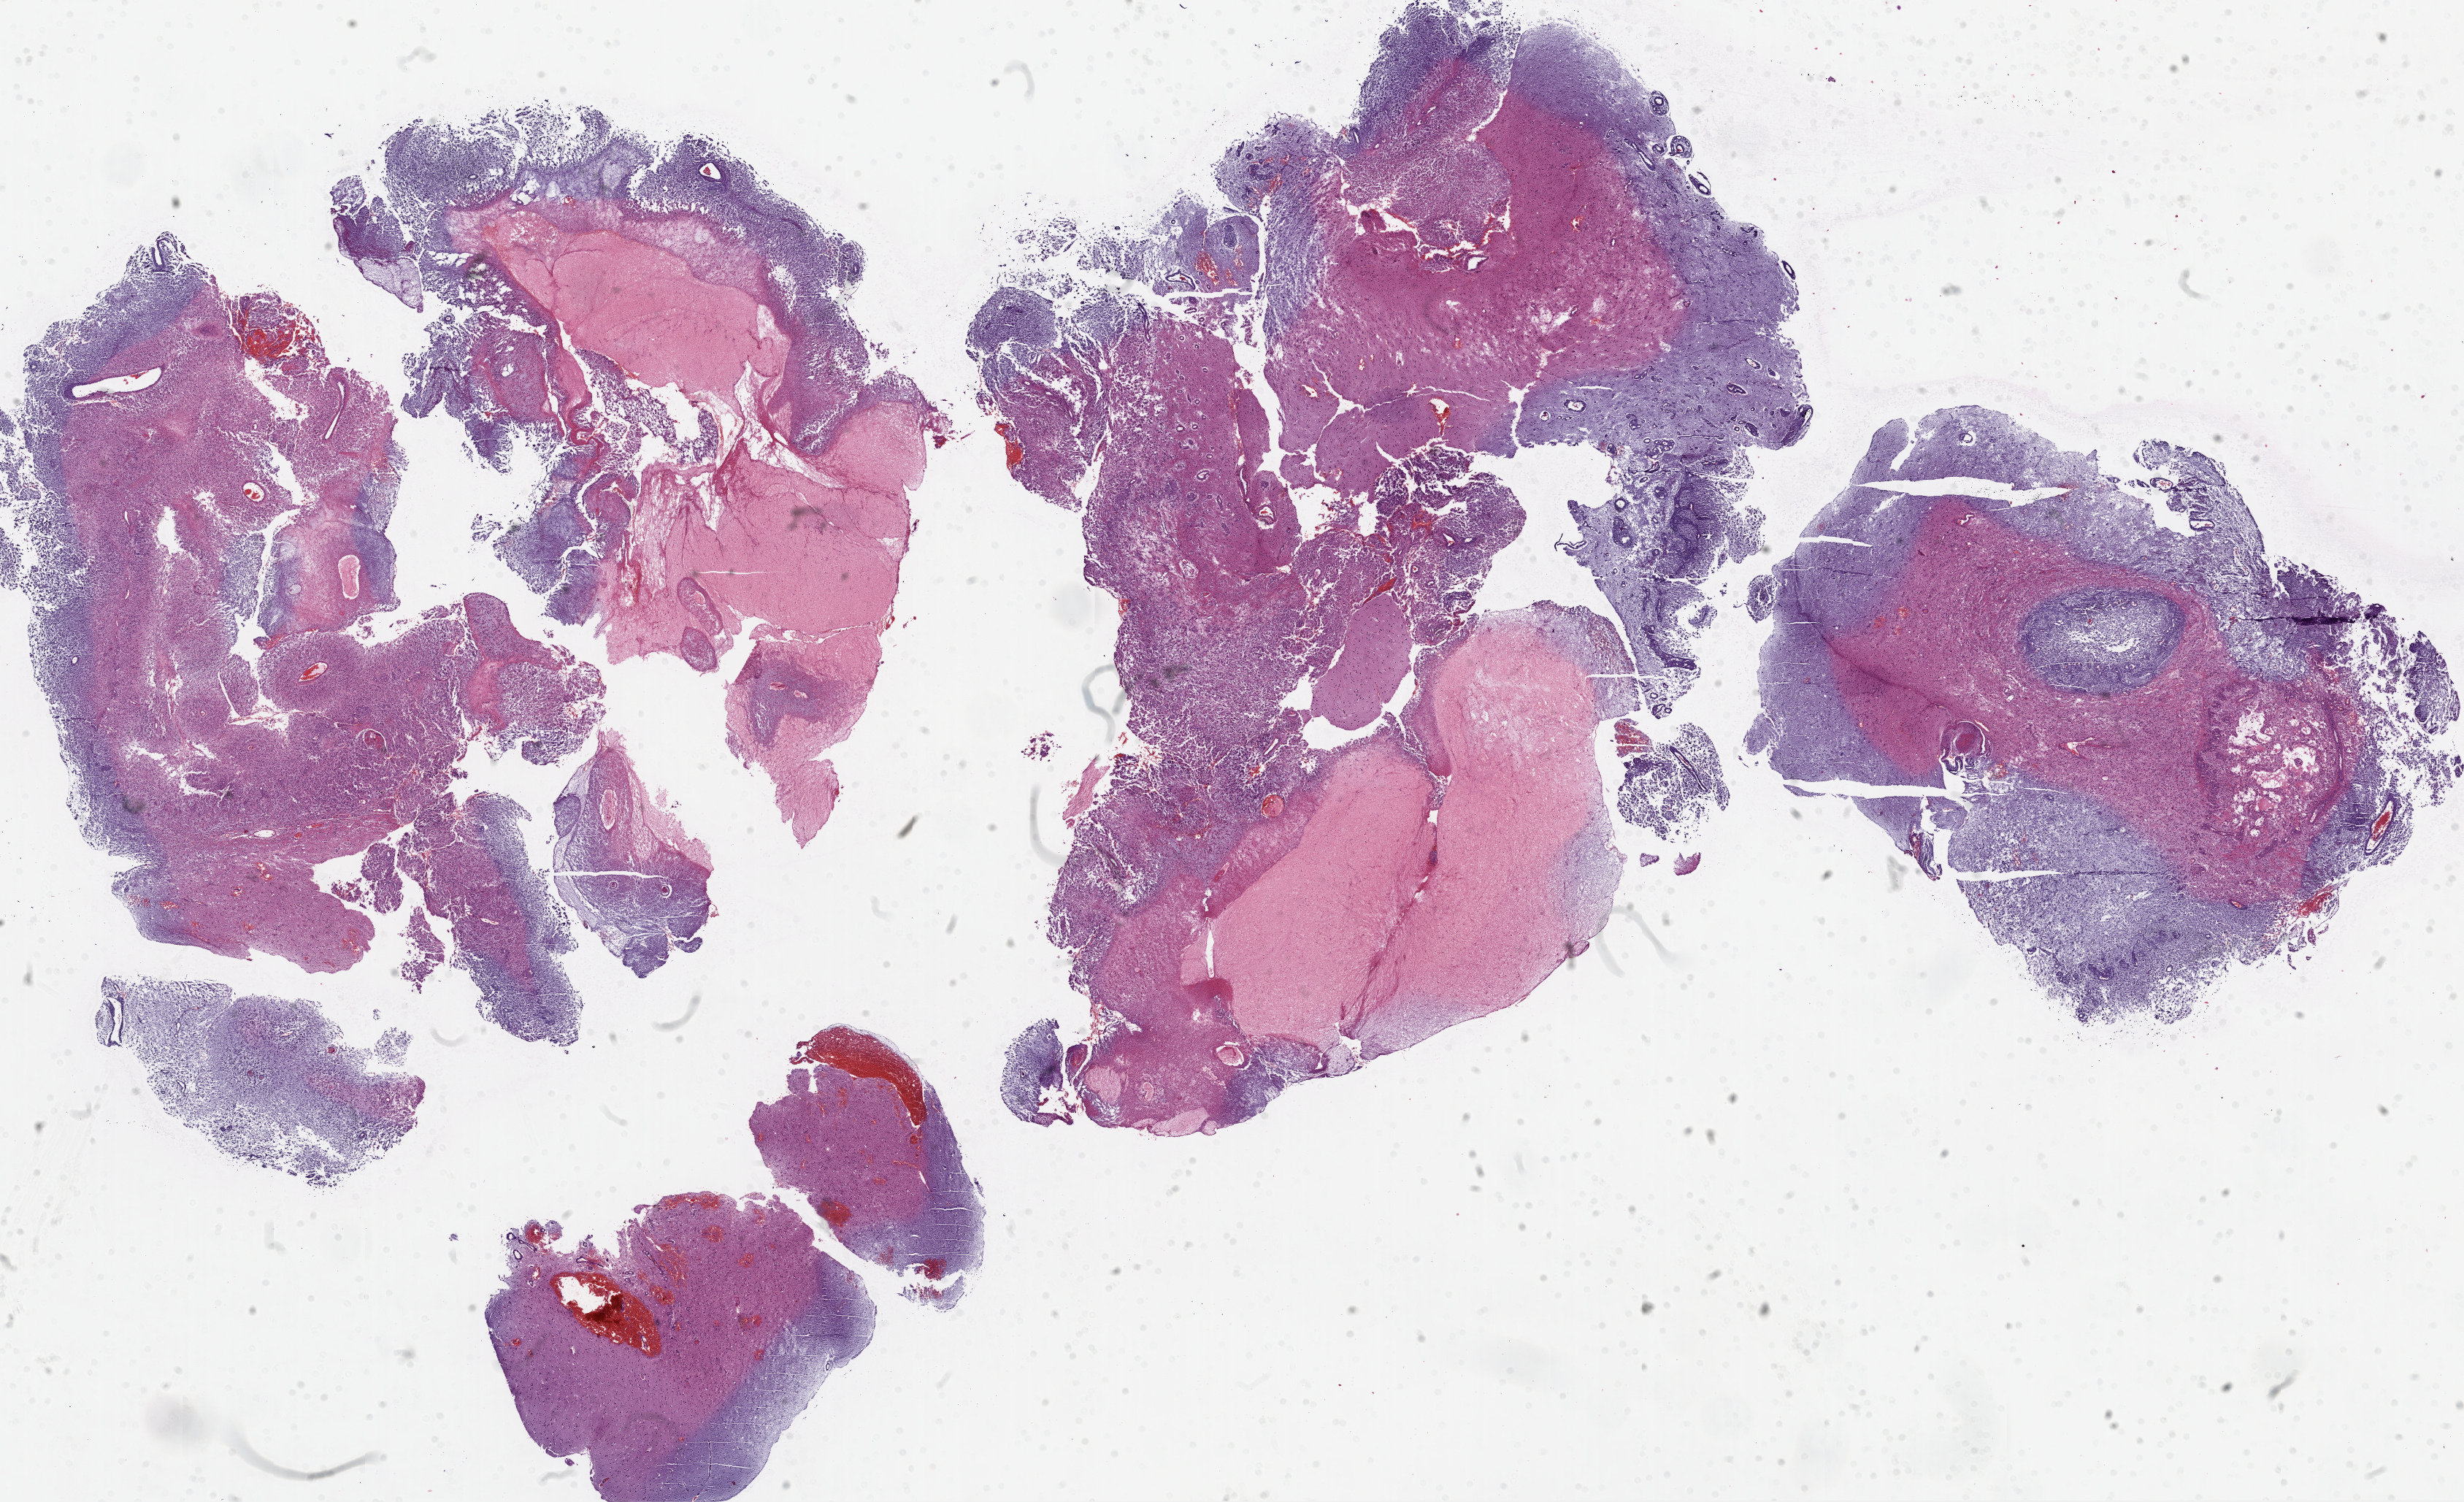
Whole-slide histology image, Hematoxylin and eosin (H&E) stained, shown as a low-resolution overview of the whole scanned area (about 27.1 x 16.5 mm, slide scanned at 20x), formalin-fixed paraffin-embedded (FFPE) diagnostic section, brain, primary tumour sample. Patient: male, age at initial diagnosis 48 years.
Pathologic diagnosis: Glioblastoma.